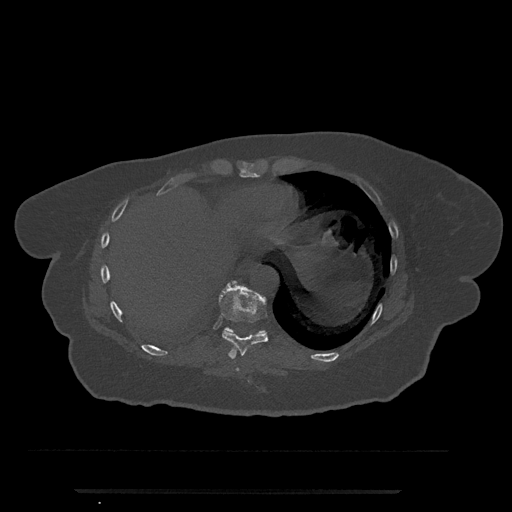
CT including the spine, one axial slice. Slice 328 of 797 in the series (ordered by position). Reconstruction kernel Br40s/3. 120 kVp. Bone window (W 1800 / L 400 HU). 0.5 mm slice thickness. 512 × 512 image matrix, field of view 440 × 440 mm. Patient: female, 51 years. Case-level facts recorded for this patient, not image findings: primary cancer: neuro.
Outlined on this slice (semi-automatic segmentation, software-assisted and operator-edited):
- T10 vertebra: bounding box <224,327,265,335> (left, top, right, bottom; pixels)
- T8 vertebra: <236,368,239,371>
- T9 vertebra: <211,281,268,359>